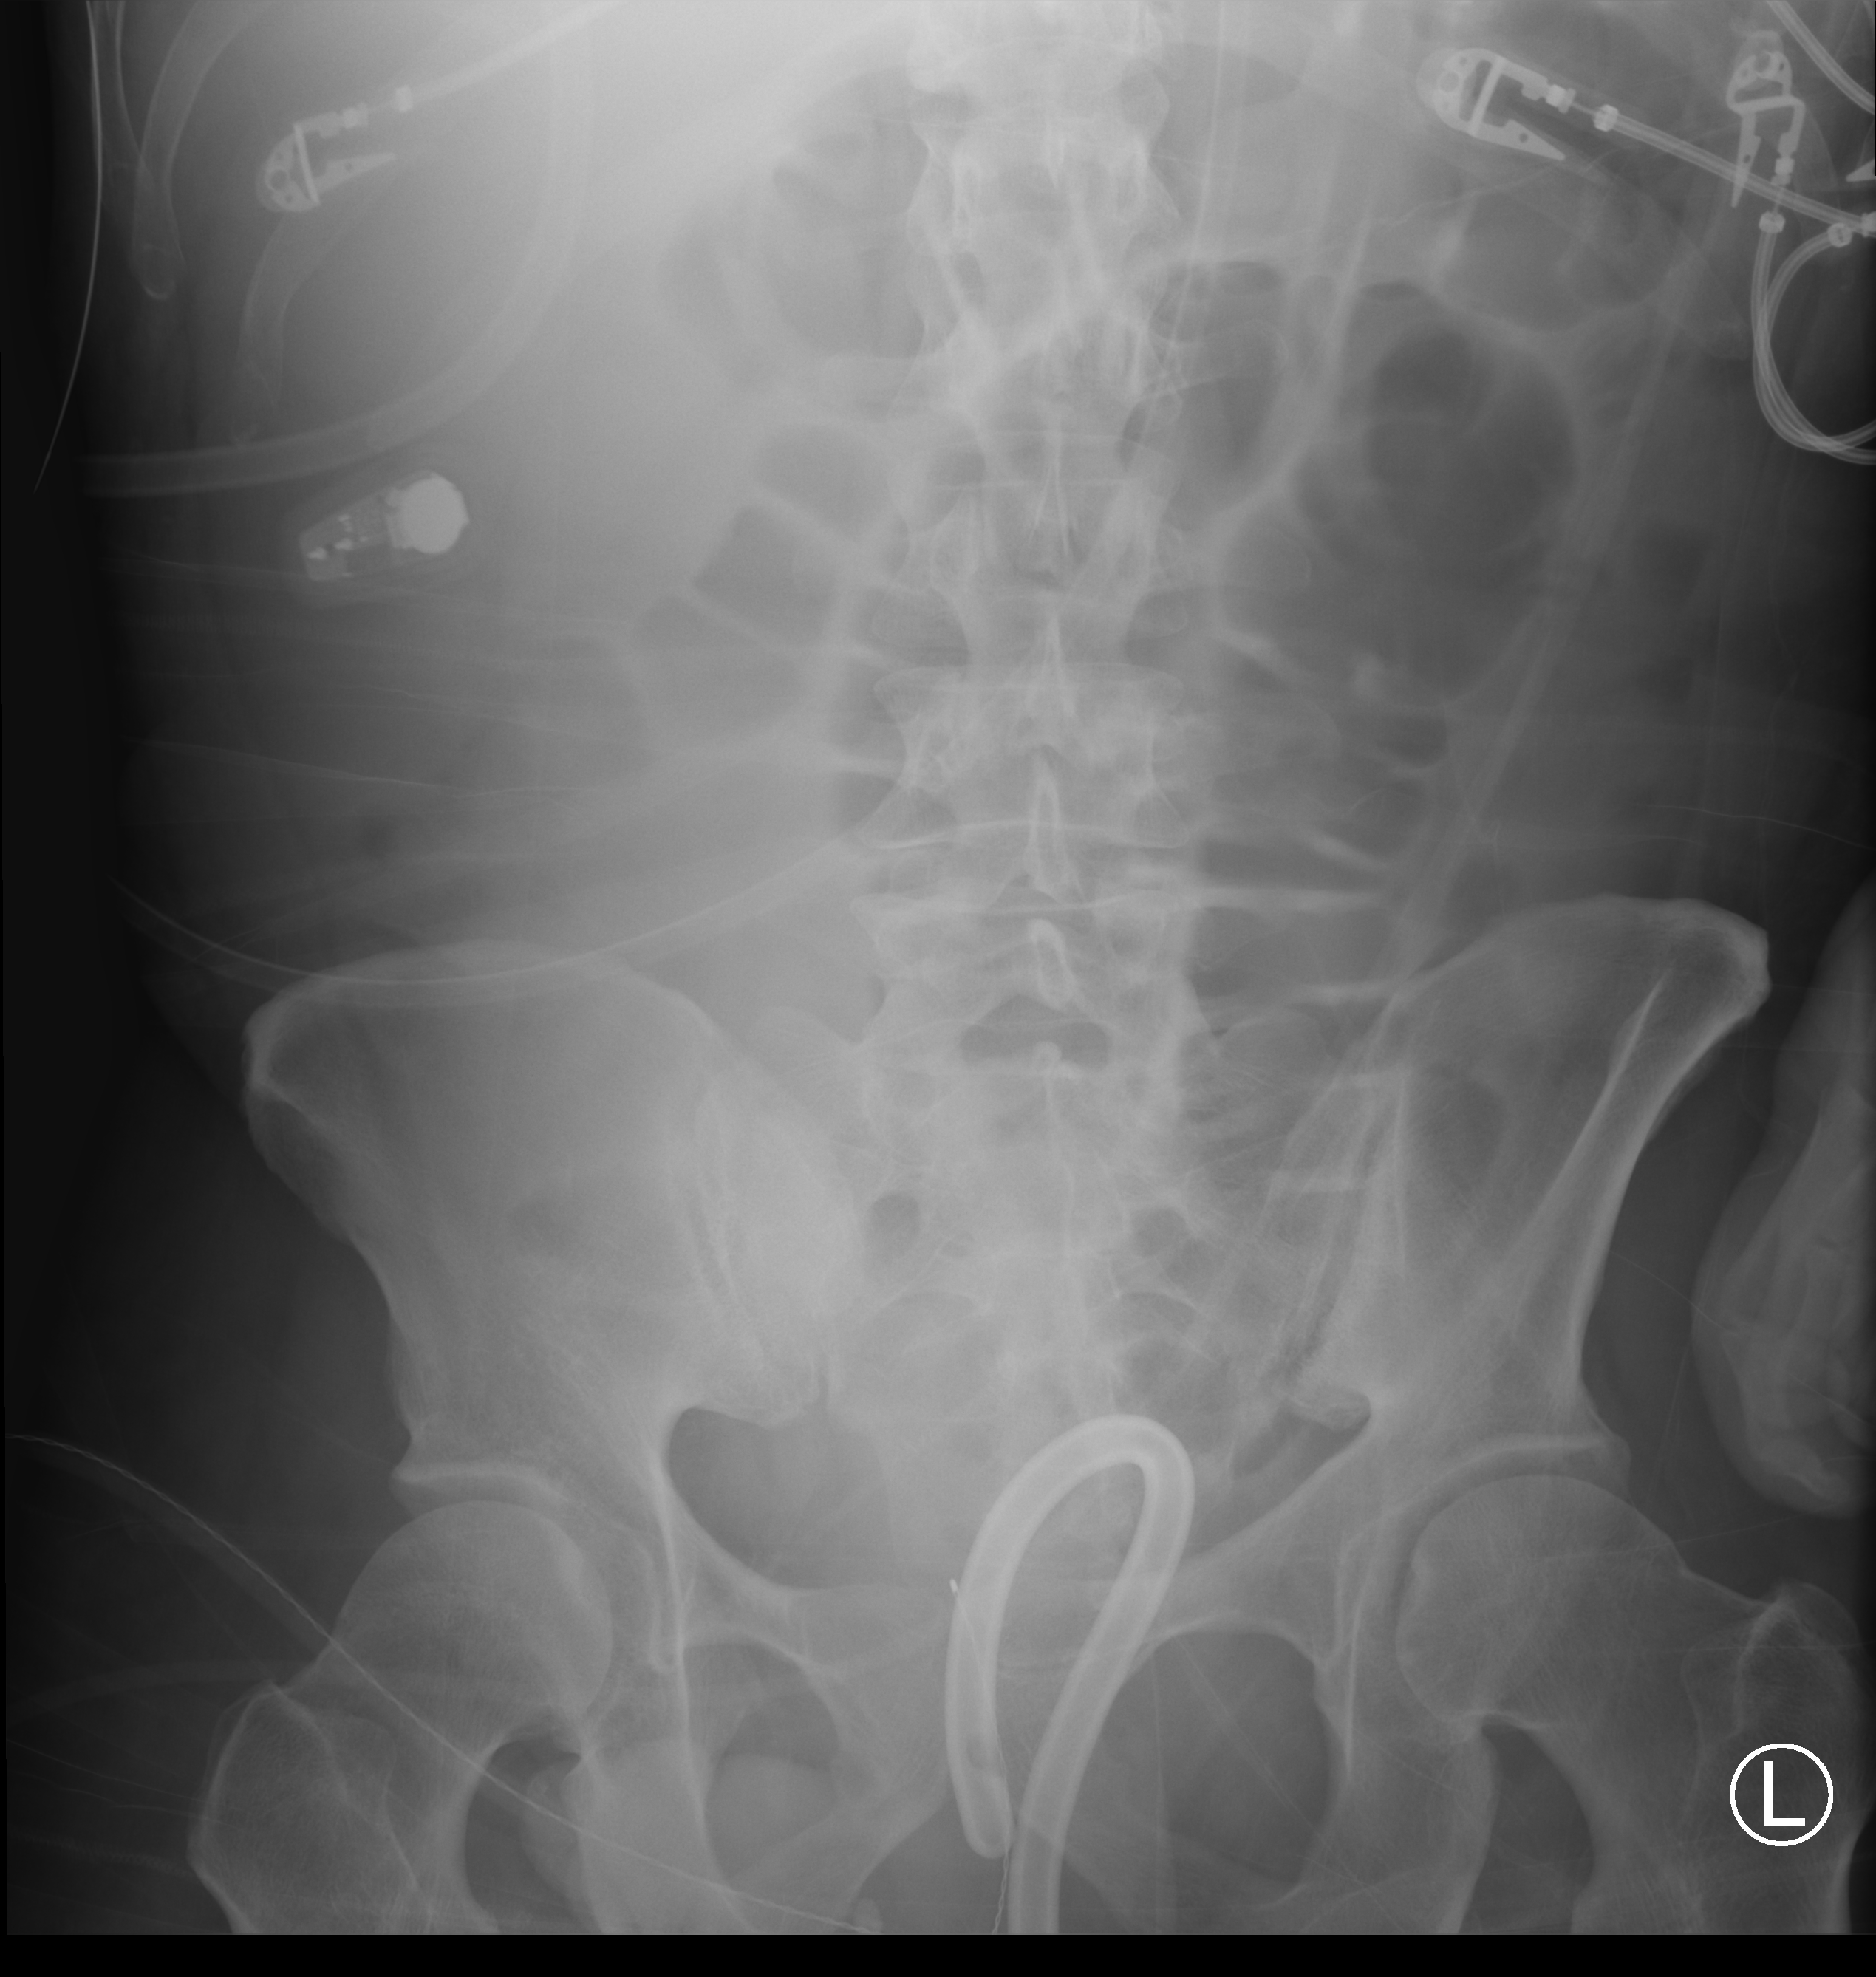
Portable abdomen radiograph, anteroposterior (AP) projection. Patient hospitalised with COVID-19; male, aged 18–59 years.
From the hospital-stay record, not from the radiograph (when in the stay this image was taken is not recorded): length of hospital stay: 96 days.